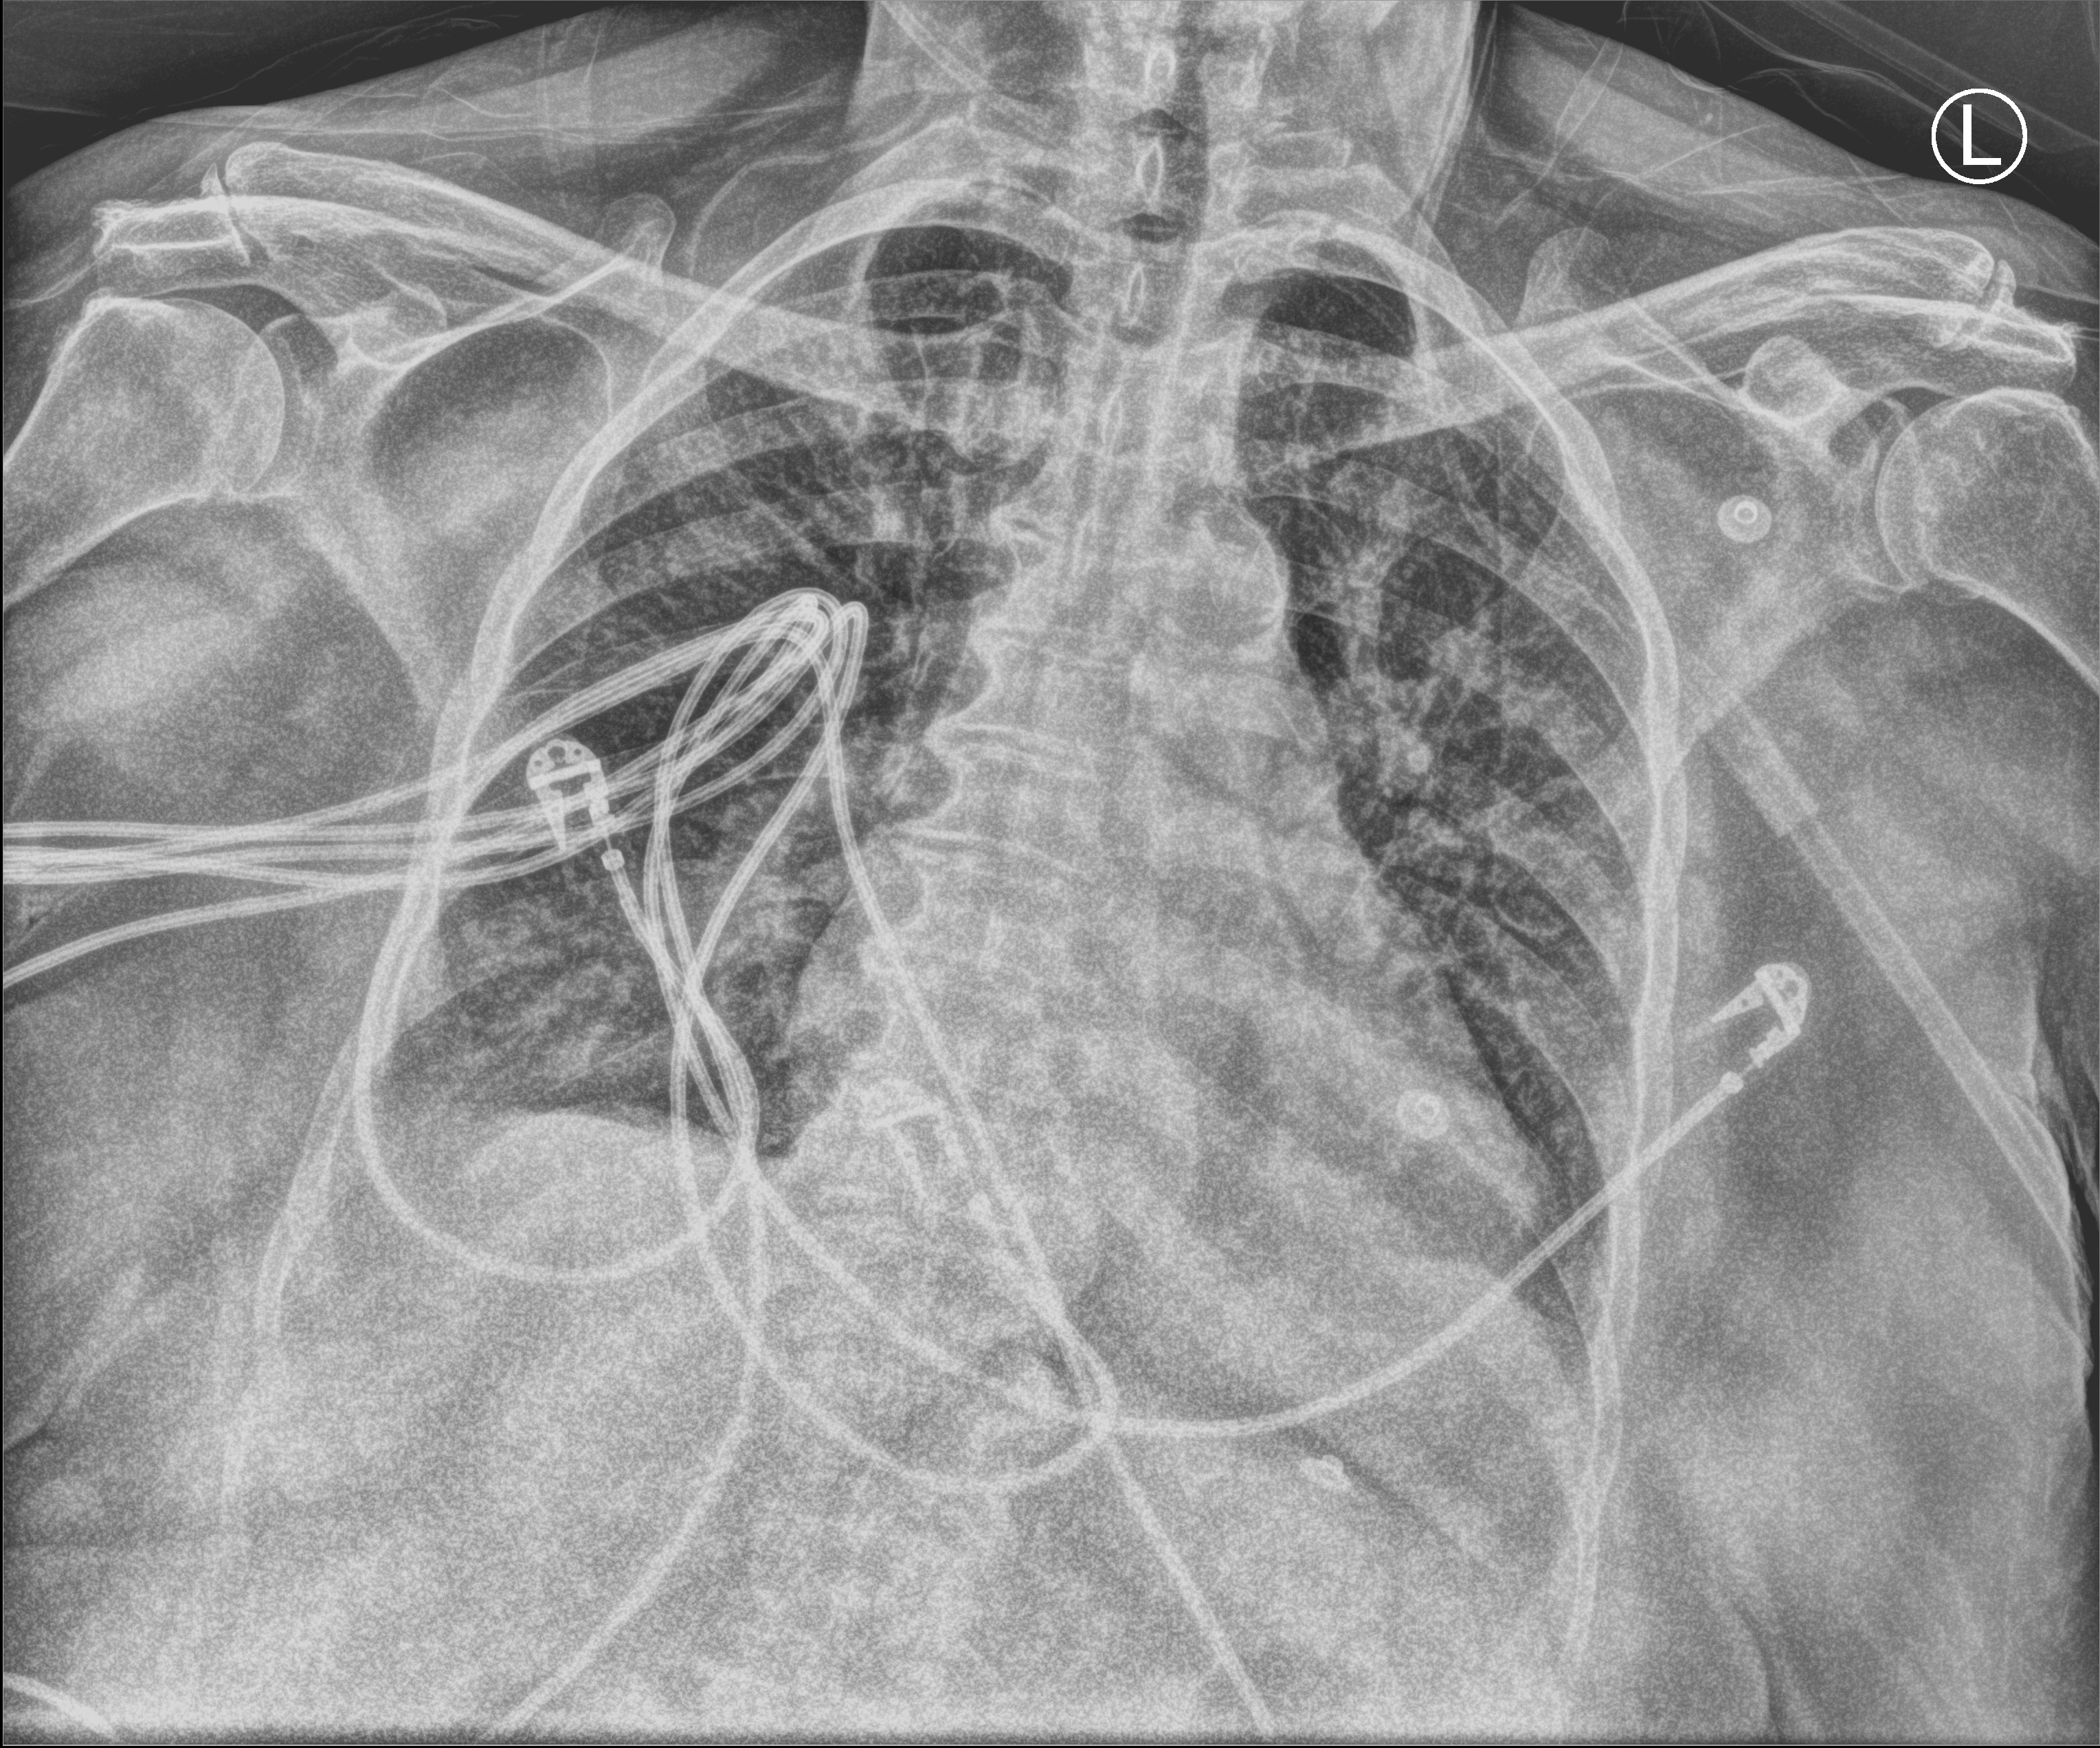
Bedside chest radiograph (computed radiography); anteroposterior (AP) projection. Female patient hospitalised with COVID-19, age 75–90 years.
Admission-level facts for this patient (not findings on this image; timing relative to this image not recorded): admitted to intensive care during this hospital stay: no; COPD (admission record): no.